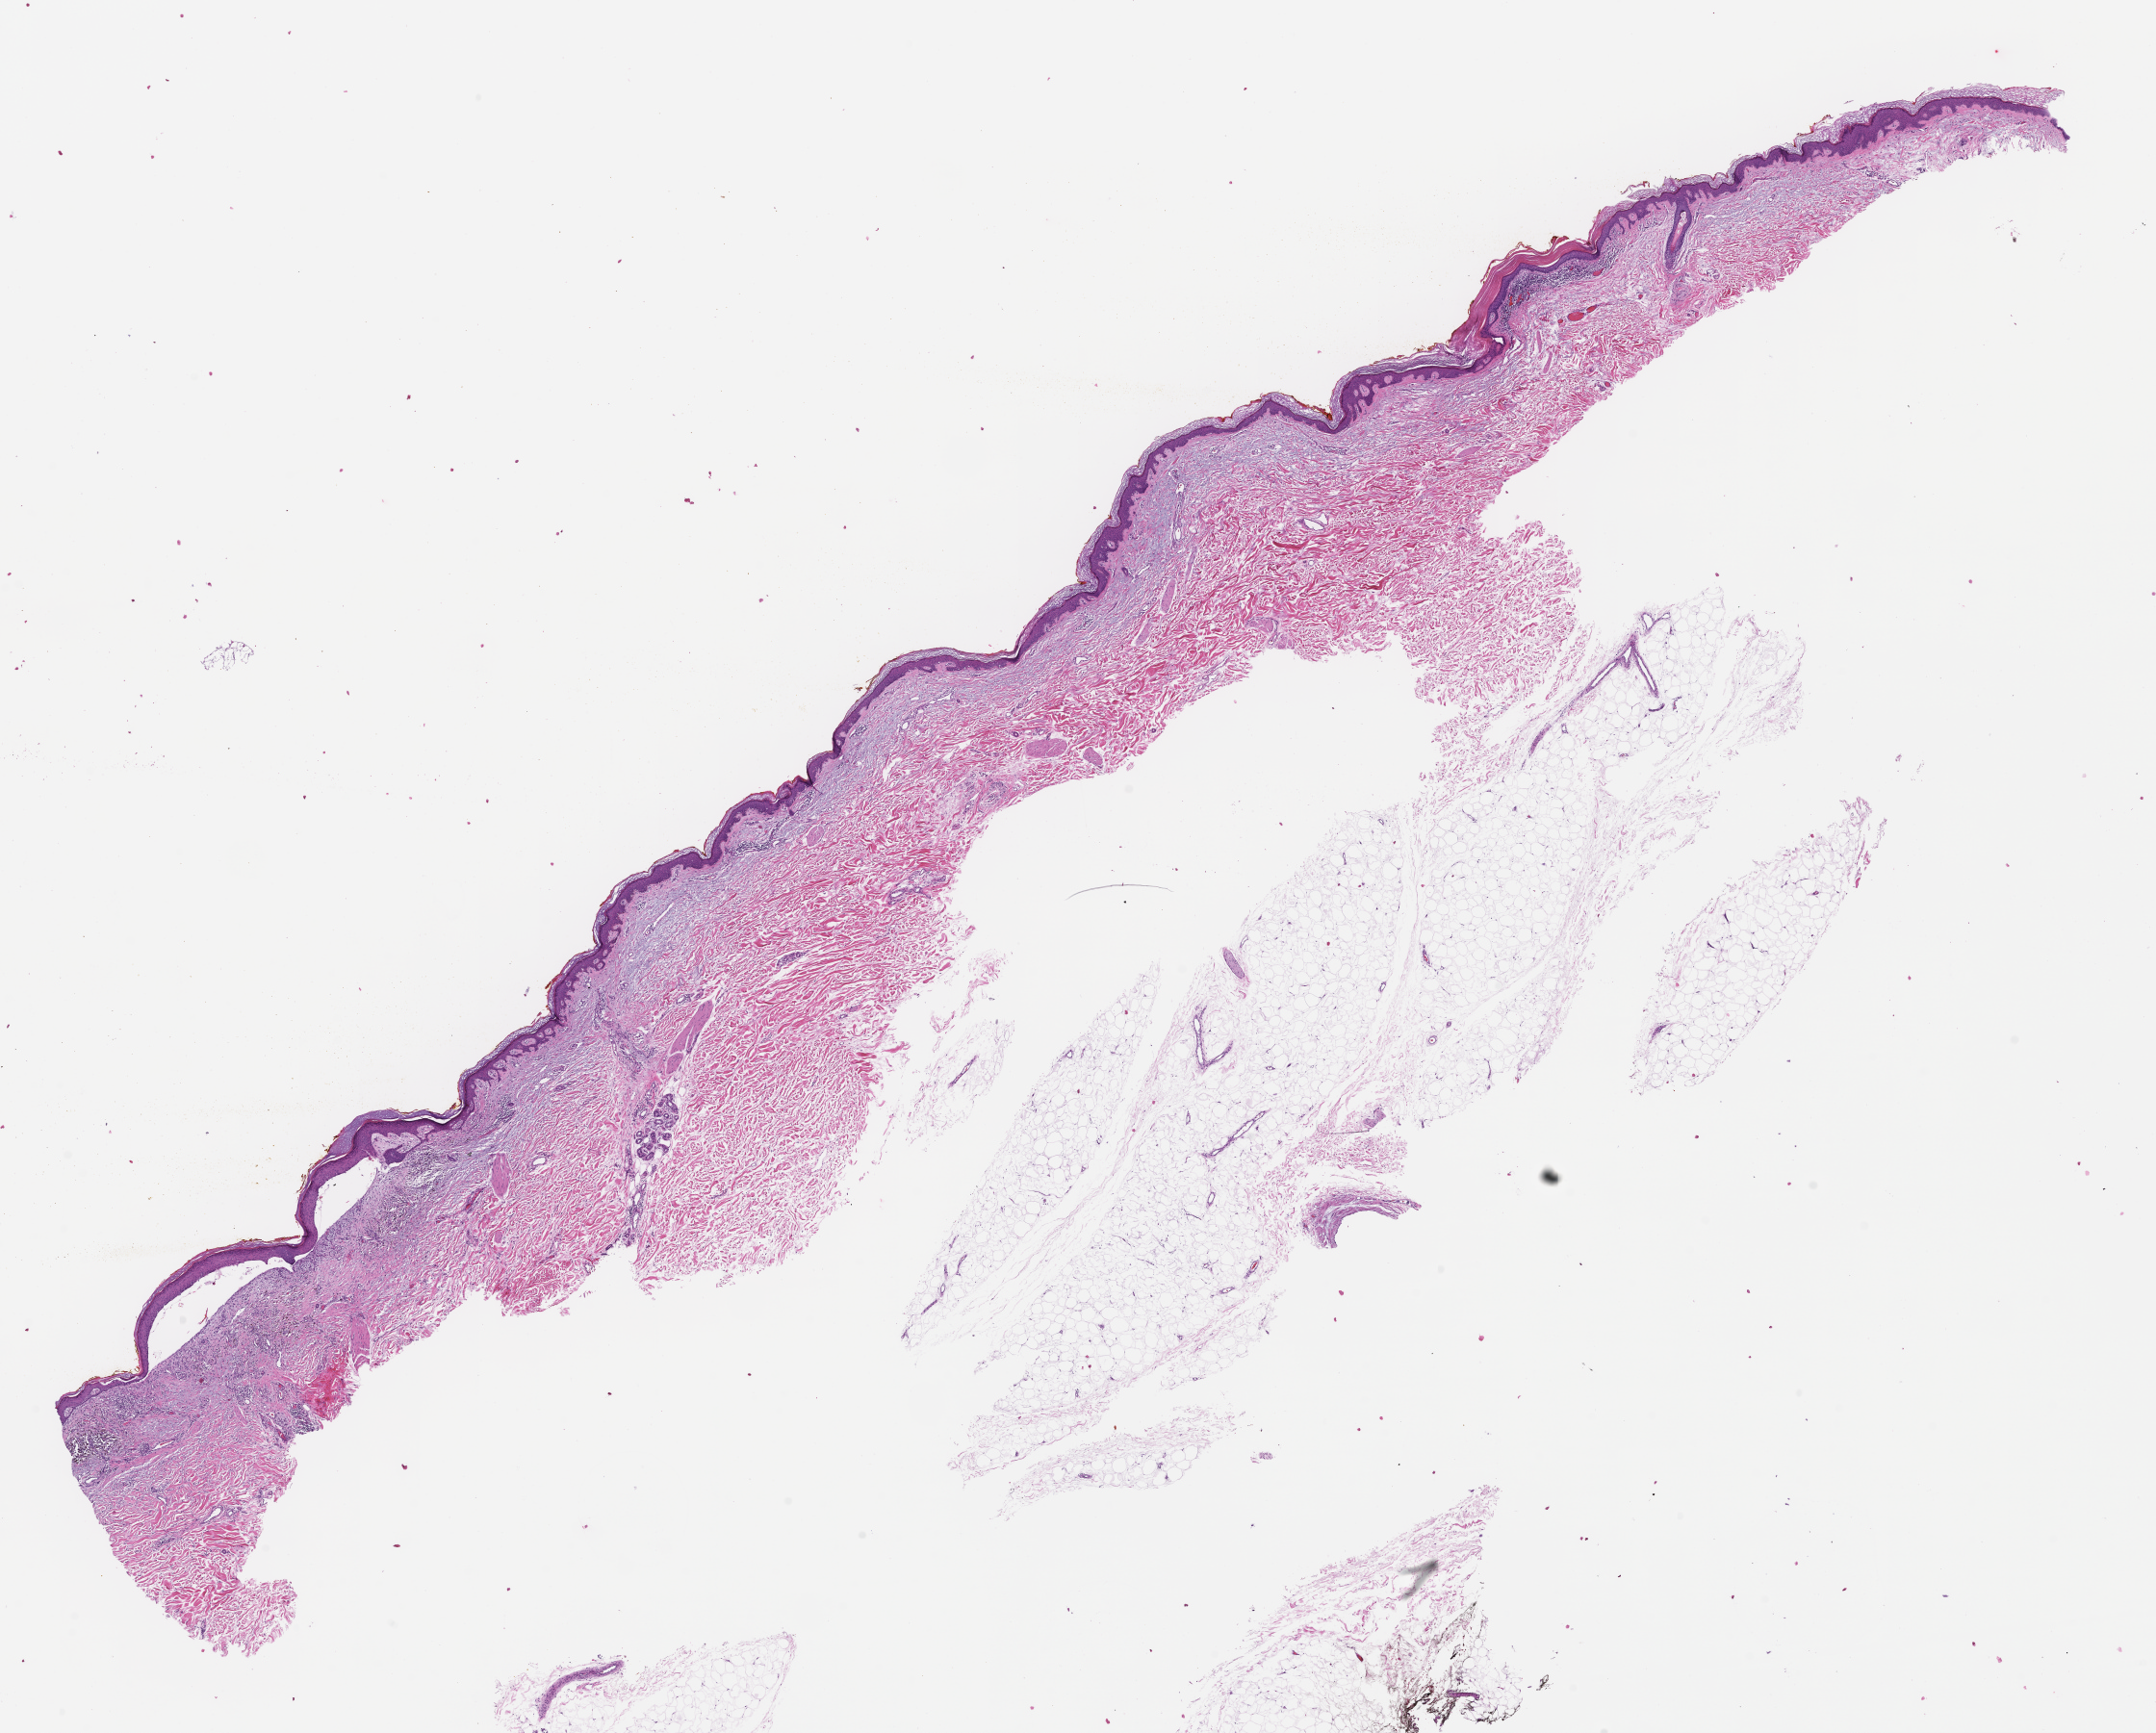
Digitized H&E-stained section — a low-resolution overview of the entire scanned area, about 18.1 x 14.5 mm; formalin-fixed paraffin-embedded section; tissue site: skin. Patient: male.
• this section: primary tumor
• diagnosis: Melanoma